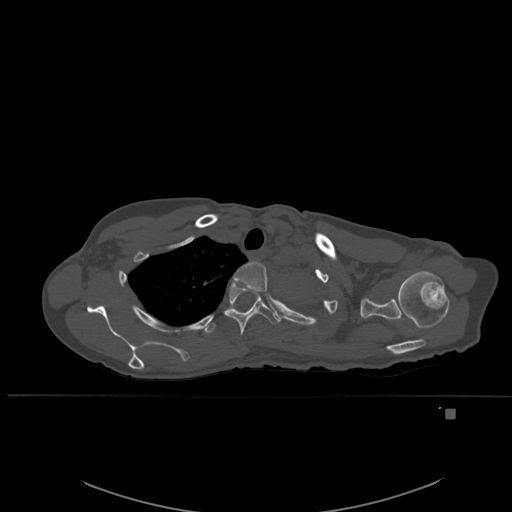
CT including the spine, one axial slice; slice 427 of 537 in the series (ordered by position); bone window (W 1800 / L 400 HU); 1.5 mm slice thickness; 512 × 512 image matrix, field of view 440 × 440 mm. Female patient, age 45 years. Case-level facts recorded for this patient, not image findings: primary cancer: lung.
Outlined on this slice (semi-automatic segmentation, software-assisted and operator-edited):
- T2 vertebra: box from (x=232, y=261) to (x=268, y=295) px
- T3 vertebra: (x=224, y=281)–(x=281, y=336)
- T4 vertebra: (x=202, y=312)–(x=224, y=334)